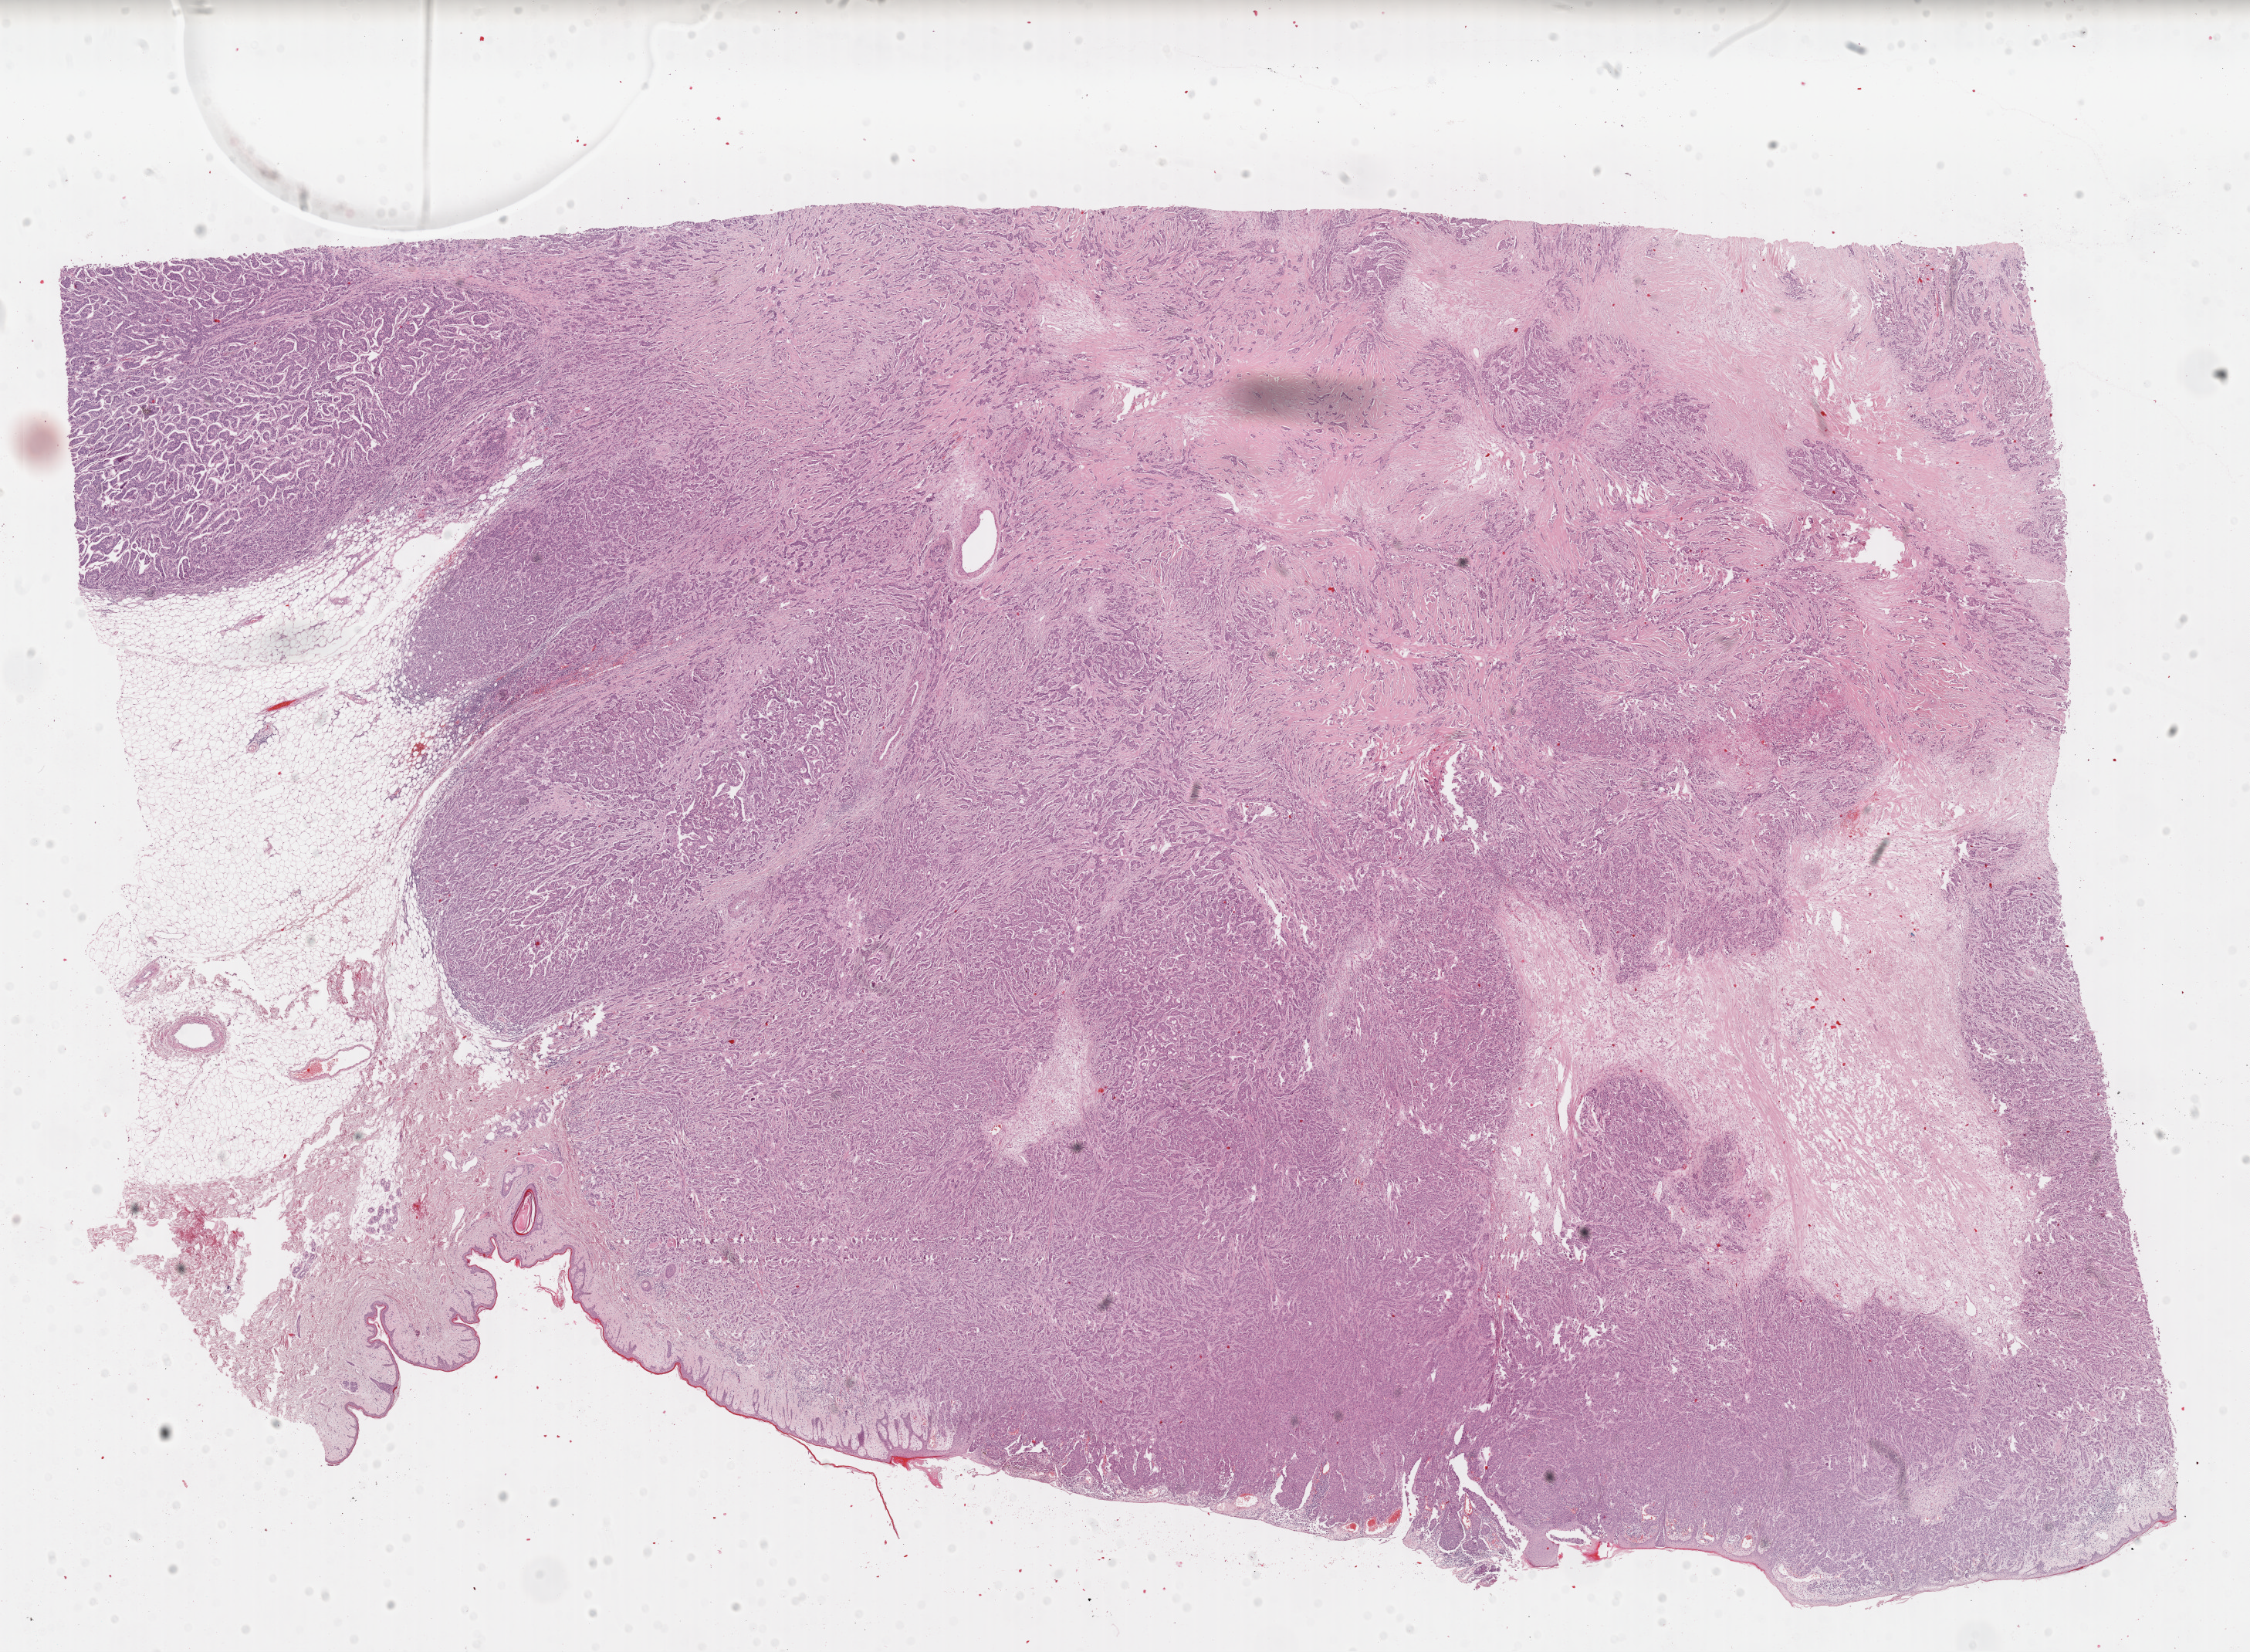
Whole-slide histology image, H&E-stained, low-resolution overview of the scanned area, about 23.0 x 16.9 mm (acquisition: 40x scan); formalin-fixed paraffin-embedded (FFPE) diagnostic section; sample: primary tumour, breast. Female patient; age at initial diagnosis 80 years.
Laterality: left. Histologic diagnosis: Infiltrating duct carcinoma, NOS. AJCC pathologic stage: IIIA (7th edition).